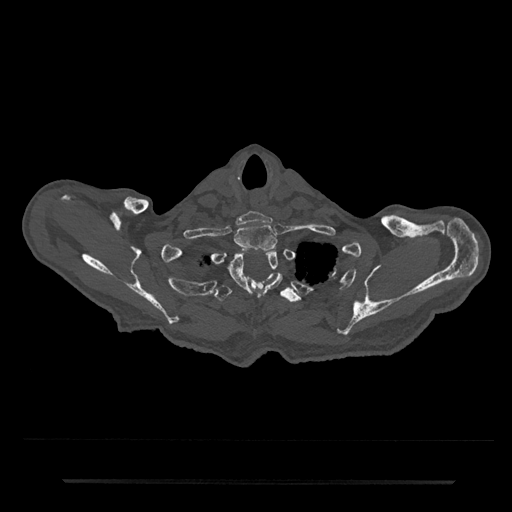
CT including the spine, one axial slice; slice 693 of 797 in the series (ordered by position); reconstruction kernel Br40s/3; 120 kVp; bone window (W 1800 / L 400 HU); 0.5 mm slice thickness; 512 × 512 image matrix, field of view 427 × 427 mm. Male patient, age 74 years. Case-level facts recorded for this patient, not image findings: primary cancer: prostate.
Annotated regions visible in this slice (semi-automatically segmented with operator editing):
- T1 vertebra: bounding box (x1, y1, x2, y2) in pixels: (234, 224, 278, 251)
- T2 vertebra: (221, 250, 283, 300)
- T3 vertebra: (214, 273, 301, 303)